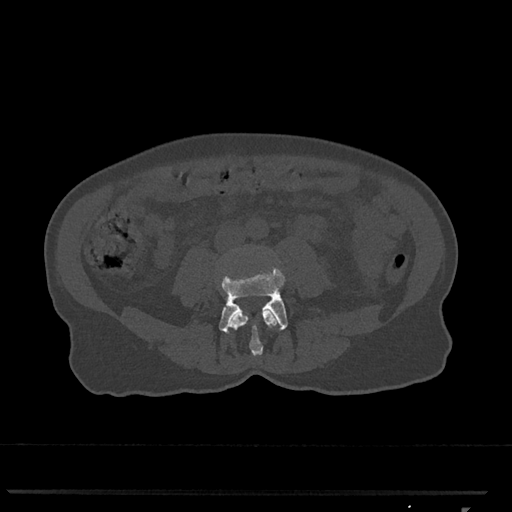
CT including the spine, one axial slice; slice 233 of 793 in the series (ordered by position); reconstruction kernel Br40s/3; bone window (W 1800 / L 400 HU); 0.5 mm slice thickness; 512 × 512 image matrix, field of view 380 × 380 mm. Female patient, age 62 years. From the clinical record (not read from this slice): primary cancer: renal.
Structures marked on this image (semi-automatic segmentation, software-assisted and operator-edited):
- L3 vertebra: box from (x=229, y=309) to (x=277, y=356) px
- L4 vertebra: (x=219, y=268)–(x=288, y=333)